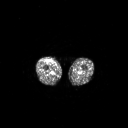
FDG PET of an extremity soft-tissue mass (from a PET/CT study), one axial slice; slice 227 of 311 in the series (ordered by position); 128 × 128 image matrix, field of view 700 × 700 mm. Male patient, age 56 years. From the clinical record (not read from this slice): histological type: pleiomorphic leiomyosarcoma; grade: intermediate; site of the primary tumour: right thigh.
Annotated regions visible in this slice (expert contour drawn on MRI and transferred to this co-registered scan by the dataset authors):
- gross tumour volume including surrounding oedema: box from (x=46, y=59) to (x=51, y=63) px